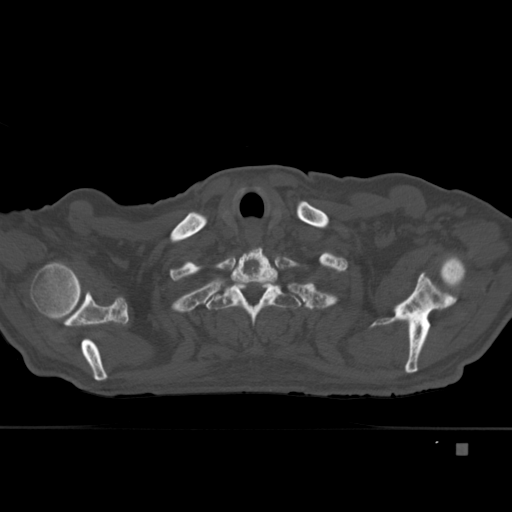
CT including the spine, one axial slice. Slice 352 of 451 in the series (ordered by position). Bone window (W 1800 / L 400 HU). 1.5 mm slice thickness. 512 × 512 image matrix, field of view 378 × 378 mm. Patient: male, 75 years. Case-level facts recorded for this patient, not image findings: primary cancer: prostate.
Structures marked on this image (semi-automatic segmentation, software-assisted and operator-edited):
- T1 vertebra: bounding box <226,247,281,300> (left, top, right, bottom; pixels)
- T2 vertebra: <201,274,301,325>